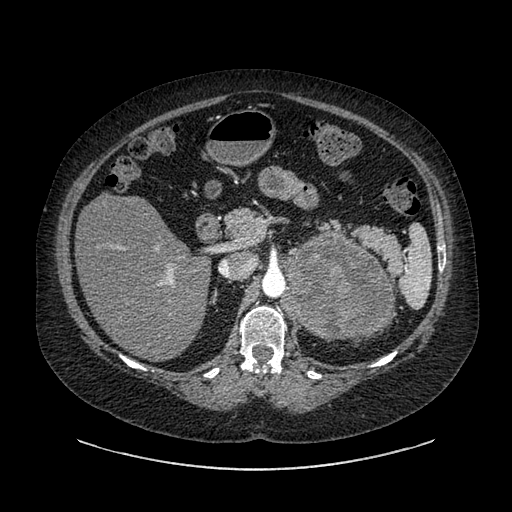
Contrast-enhanced abdominal CT, one axial slice. Position 565 of 769 along the scan axis. Intravenous contrast given. Soft-tissue window (W 400 / L 40 HU). 0.62 mm slice thickness. 512 × 512 image matrix. Female patient, age 61 years. From the clinical record (not read from this slice): diagnosis: adrenocortical carcinoma; tumour side: left adrenal; tumour size at pathology: 13 cm.
Annotated regions visible in this slice (semi-automatically segmented with operator editing):
- mass: bounding box [x1, y1, x2, y2] px = [284, 232, 391, 340]